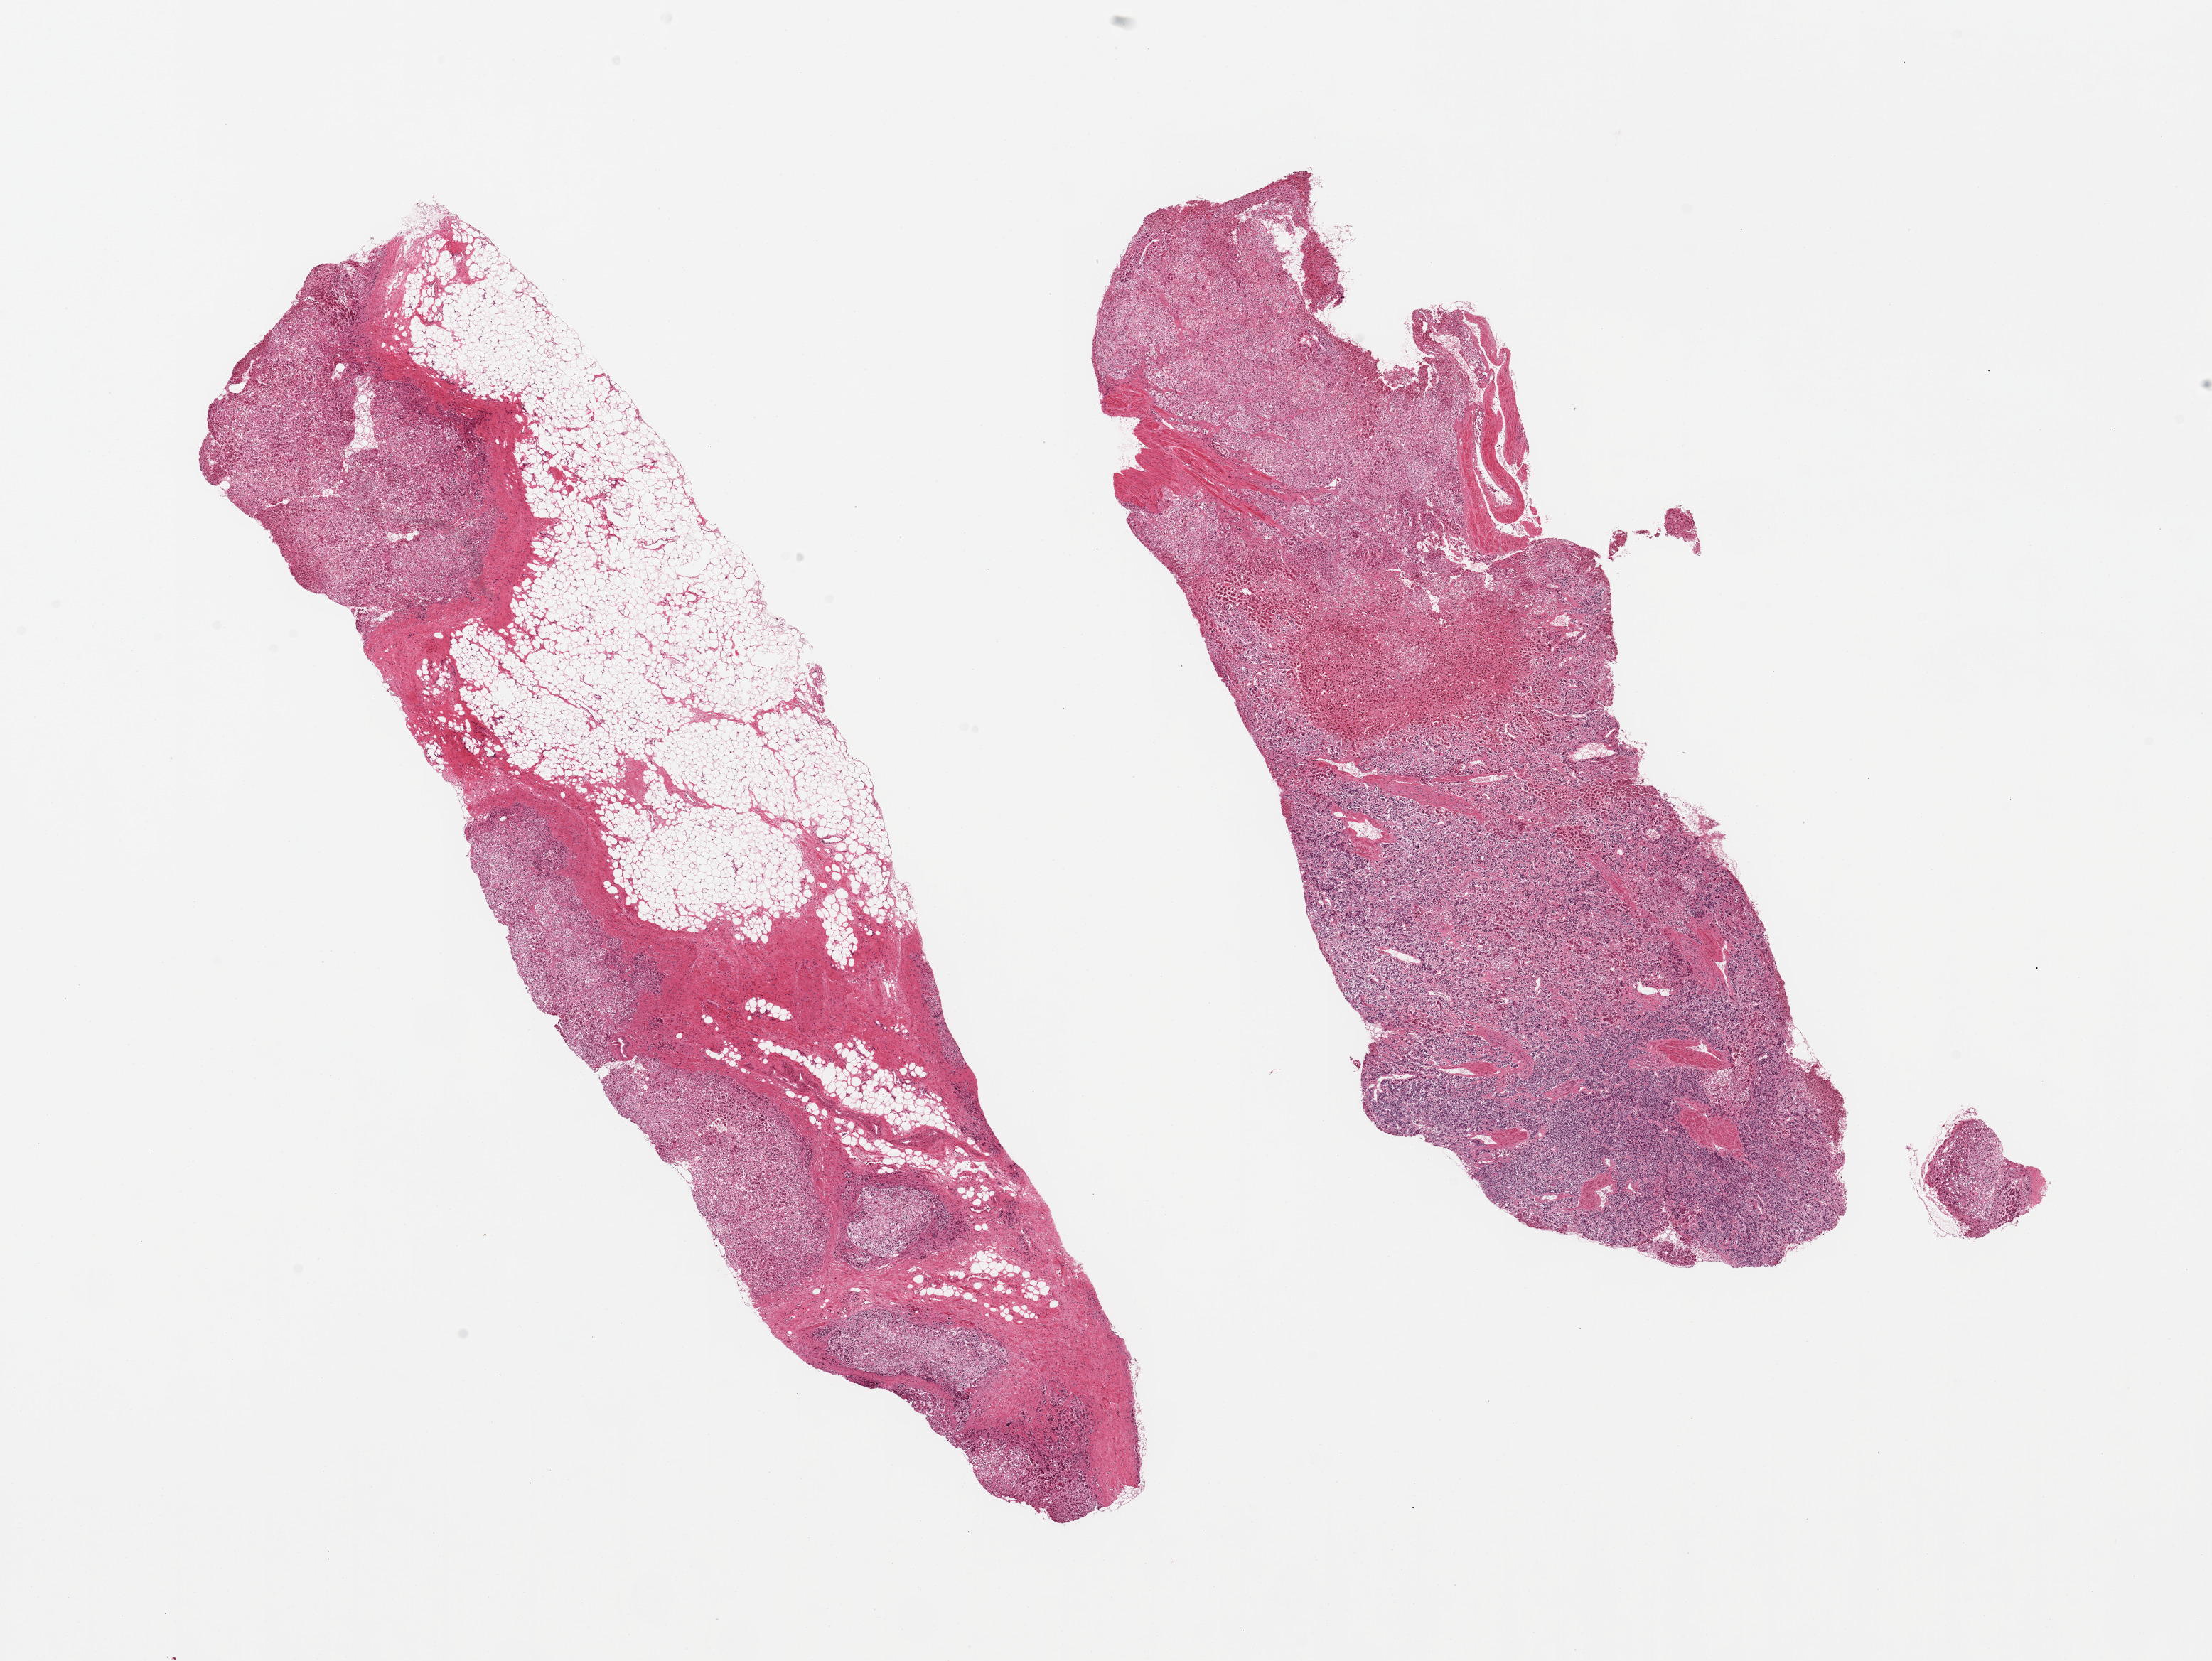
H&E whole-slide image, low-resolution overview of the scanned area, about 24.6 x 18.5 mm (acquisition: 20x scan), PAXgene-fixed, paraffin-embedded tissue, section of adrenal gland (target tissue), donor tissue sample. Donor sex: male.
Pathologist's review note for this sample: 2 pieces; cortex and medulla, 70% of one piece is fat and adrenal capsule.